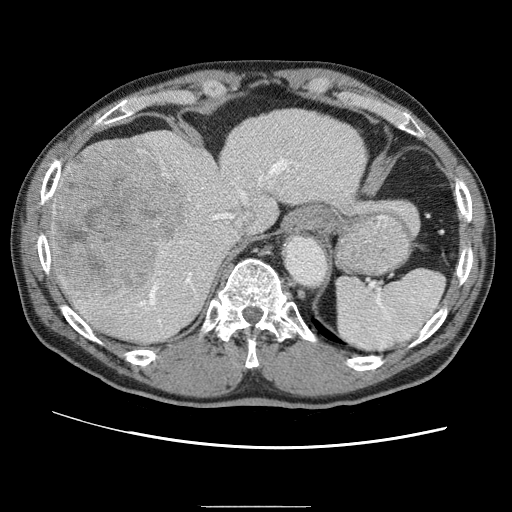
Contrast-enhanced abdominal CT (liver protocol), one axial slice. Position 48 of 75 along the scan axis. One of 2 acquisitions stored at this slice position. Soft-tissue window (W 400 / L 40 HU). 2.5 mm slice thickness. 512 × 512 image matrix. Case-level facts recorded for this patient, not image findings: diagnosis: hepatocellular carcinoma (patient treated with transarterial chemoembolisation; whether this scan precedes or follows treatment is not stated here); TNM stage (as recorded): Stage-II; Child-Pugh class: A; tumour differentiation: well differentiated; tumour size: 2 cm.
Structures marked on this image (semi-automatically segmented with operator editing):
- abdominal aorta: box from (x=282, y=236) to (x=325, y=286) px
- liver parenchyma outside the tumour (the mass and vessels are separate outlines, so this box may not span the whole liver): (x=48, y=110)–(x=372, y=342)
- mass: (x=50, y=143)–(x=188, y=300)
- liver vessels: (x=144, y=157)–(x=290, y=306)